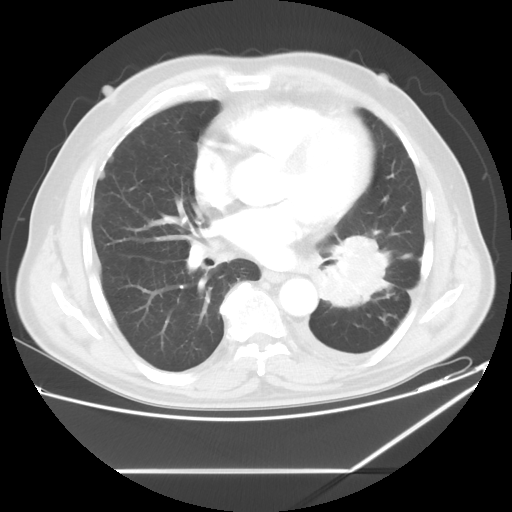
Chest CT, one axial slice. Slice 28 of 60 in the series (ordered by position). 120 kVp. Lung window (W 1500 / L -600 HU). 512 × 512 image matrix. Male patient, age 62 years. From the clinical record (not read from this slice): clinical TNM (as recorded): T3 N0 M1.
Structures marked on this image (bounding box drawn by a radiologist):
- lung tumour (recorded histology: adenocarcinoma): bounding box (x1, y1, x2, y2) in pixels: (312, 228, 393, 311)
- lung tumour (recorded histology: adenocarcinoma): (320, 236, 393, 312)